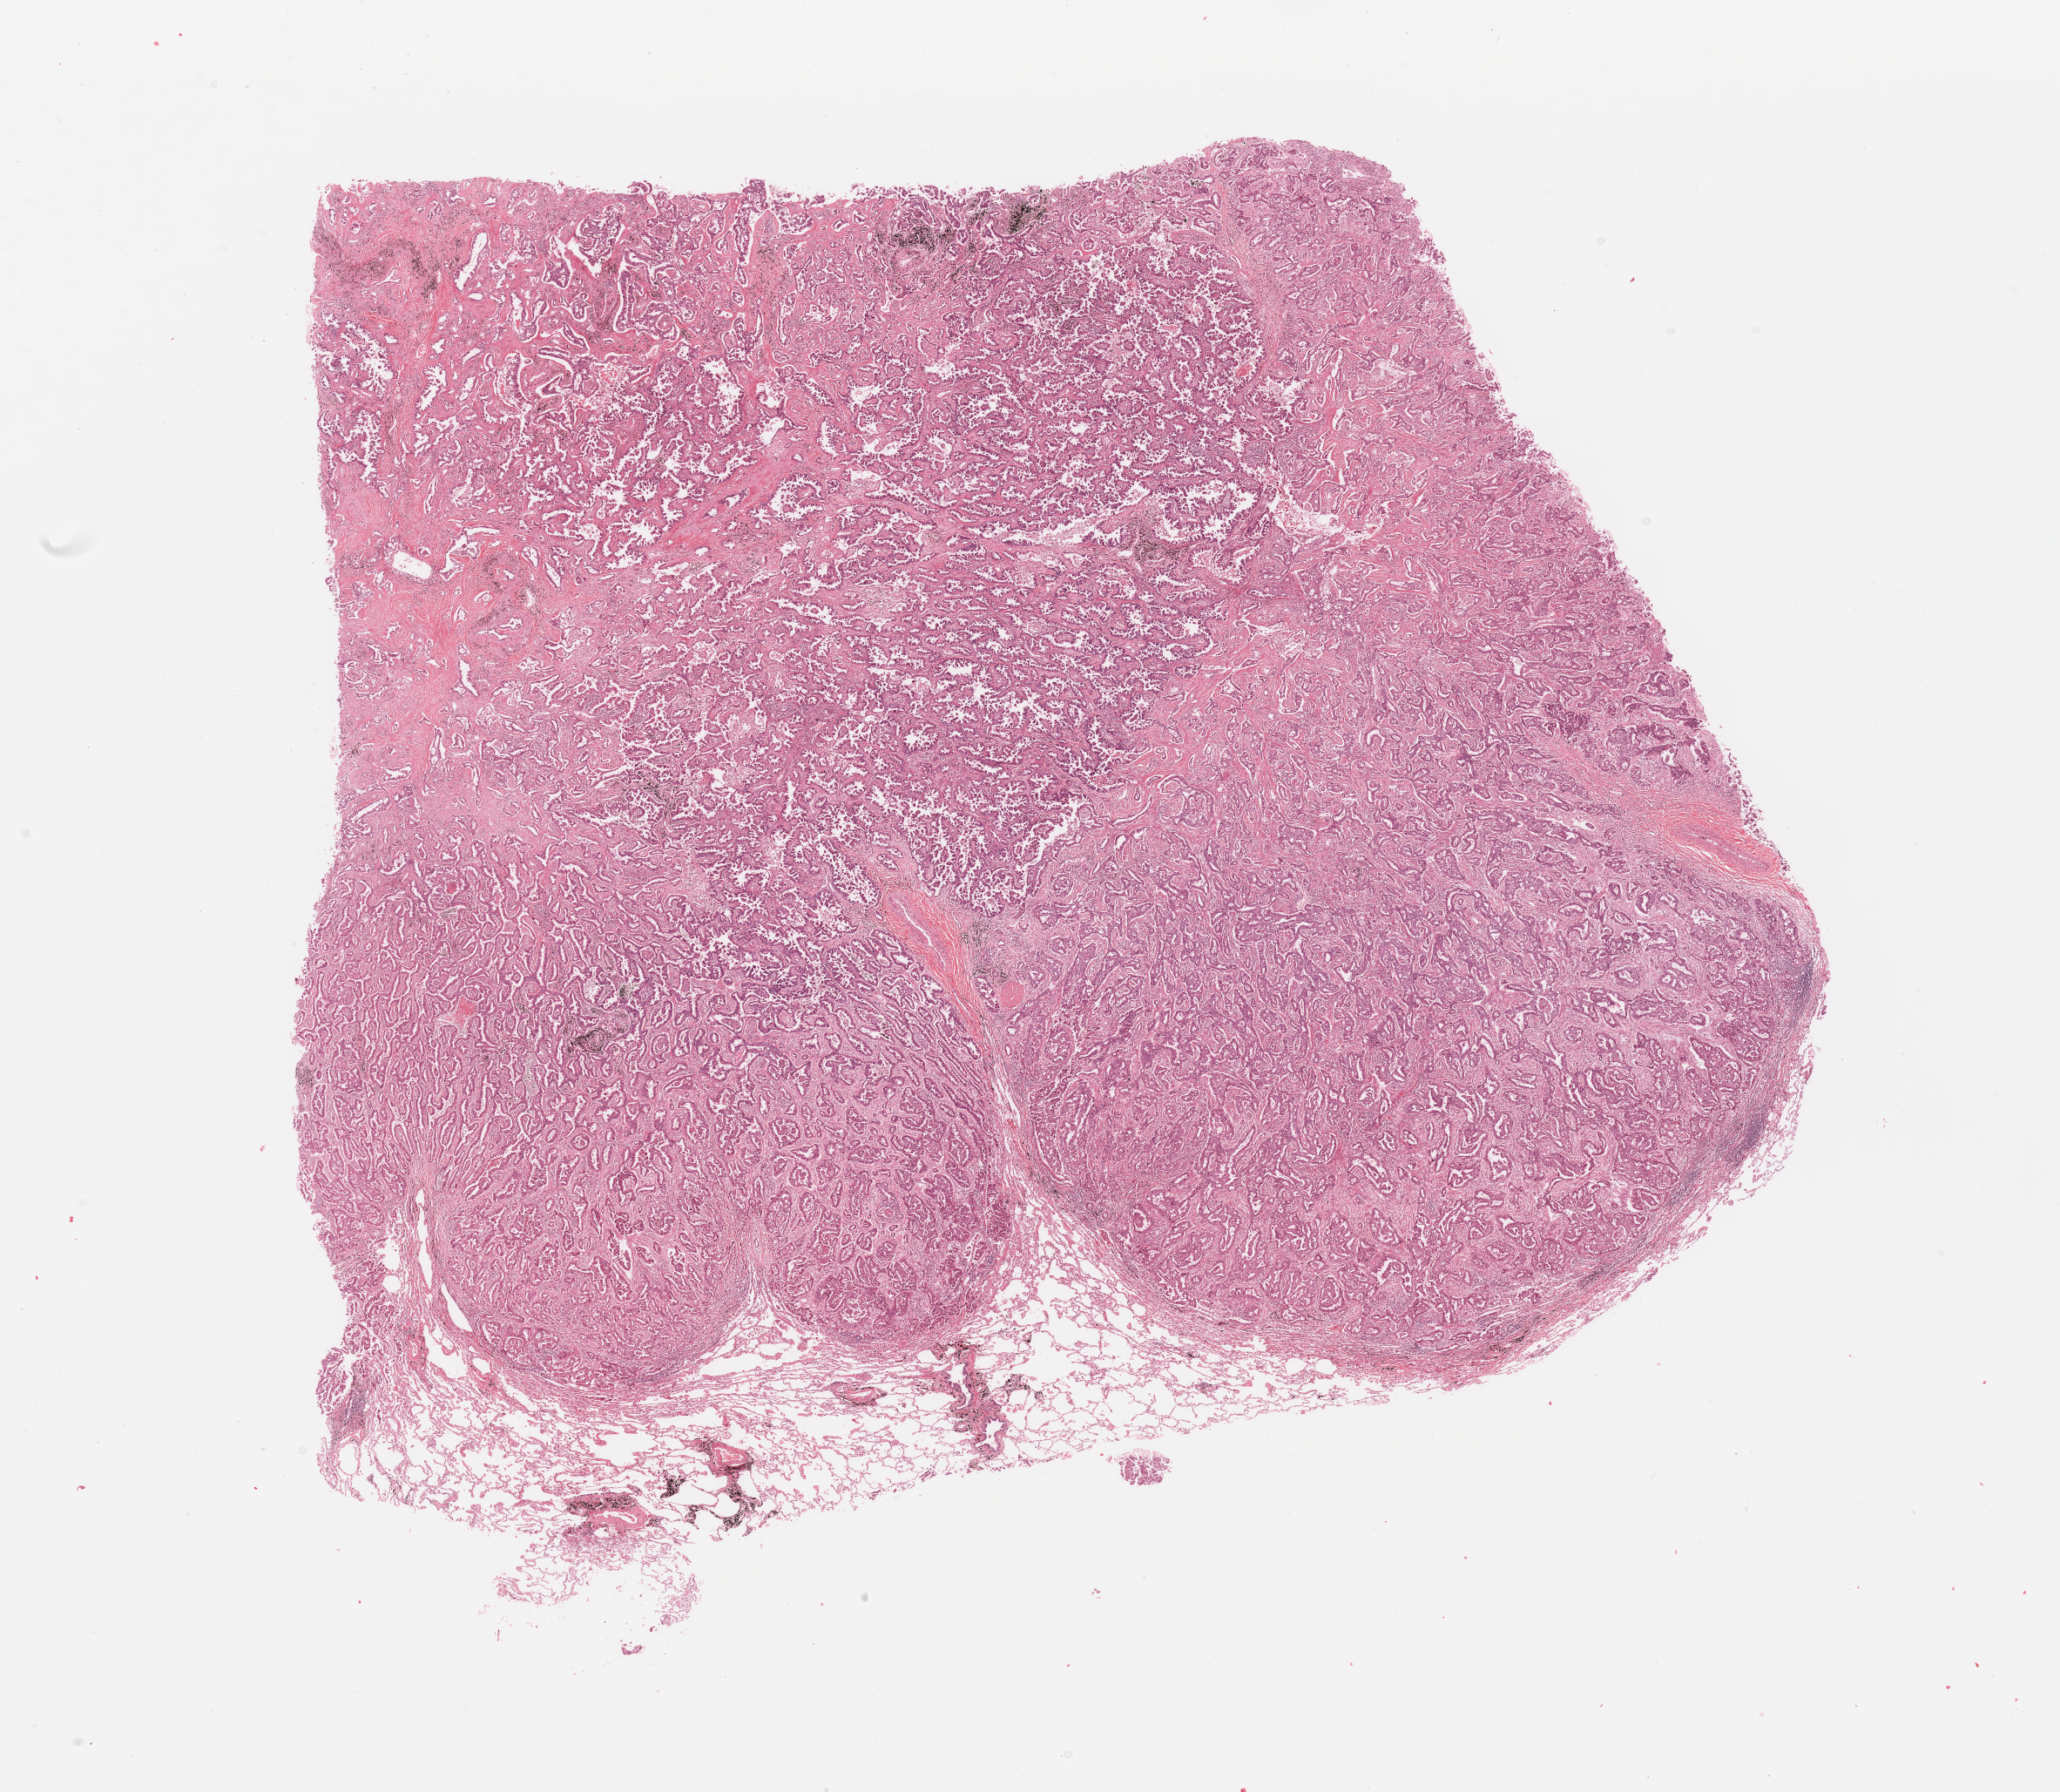
Digitized H&E-stained tissue section (whole slide) — whole scanned area (about 18.7 x 16.3 mm) shown as a low-resolution overview; tumour tissue sample, sampled site: lung. Female, 55 y/o. Histologic grade: G2 (moderately differentiated). Slide review estimates, as recorded: tumour nuclei 70%, necrosis 5%.
Diagnosis: Adenocarcinoma, NOS. AJCC pathologic stage: IA.